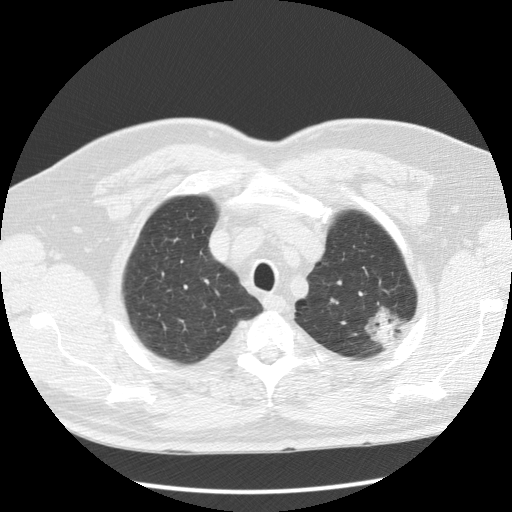
Axial slice from a low-dose chest CT screening exam; first (baseline) screen; lung window (W 1500 / L -600 HU); 2.5 mm slice thickness; standard (soft-tissue) reconstruction kernel (STANDARD). Male, age 60 years at enrolment.
• Expert reader's lesion annotation, bounding box (x1, y1, x2, y2) in pixels: (352, 295, 414, 355).
• The screening reader recorded 3 non-calcified nodules or masses ≥4 mm on this exam; which of them this box marks is not recorded.
• Later outcome: lung cancer diagnosed 48 days after this screen — bronchiolo-alveolar adenocarcinoma, NOS, left upper lobe, well differentiated (G1), stage IA (AJCC 6th edition), 27 mm at pathology.